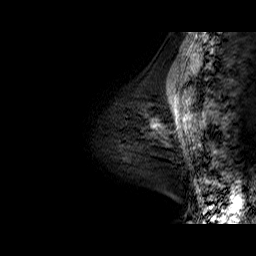
Breast MRI (dynamic contrast-enhanced), one sagittal slice; slice 16 of 60 in the series (ordered by position); dynamic contrast-enhanced series, time point 2 of 6 at this slice position (early post-contrast); 1.5 T; TE 6.4 ms, TR 32.9 ms; 4 mm slice thickness; 256 × 256 image matrix, field of view 200 × 200 mm. Female patient. Case-level facts recorded for this patient, not image findings: setting: breast cancer imaged before/during neoadjuvant chemotherapy; receptor status: HR-positive, HER2-negative.
Structures marked on this image (semi-automatic segmentation, software-assisted and operator-edited):
- analysis volume of interest (the breast-tissue region the enhancement analysis was run in; not a lesion): box from (x=106, y=86) to (x=164, y=171) px
- tumour enhancement mask (voxels above the 100 % enhancement threshold inside the analysis volume of interest): (x=153, y=125)–(x=156, y=128)